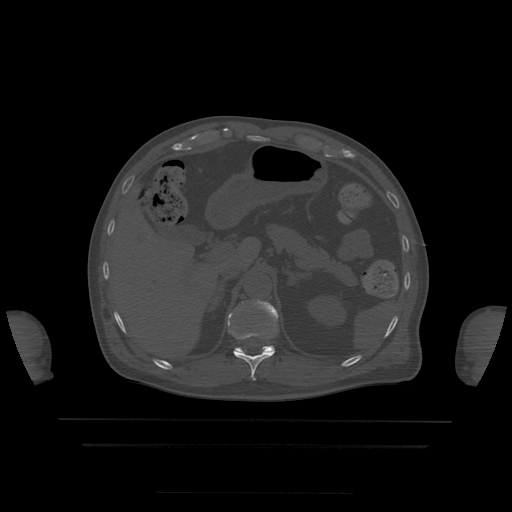
CT including the spine, one axial slice; position 211 of 522 along the scan axis; bone window (W 1800 / L 400 HU); 1.25 mm slice thickness; 512 × 512 image matrix. Patient age 68 years. From the clinical record (not read from this slice): primary cancer: urothelial.
Outlined on this slice (semi-automatically segmented with operator editing):
- T11 vertebra: box from (x=228, y=314) to (x=275, y=380) px
- T12 vertebra: (x=235, y=301)–(x=279, y=354)